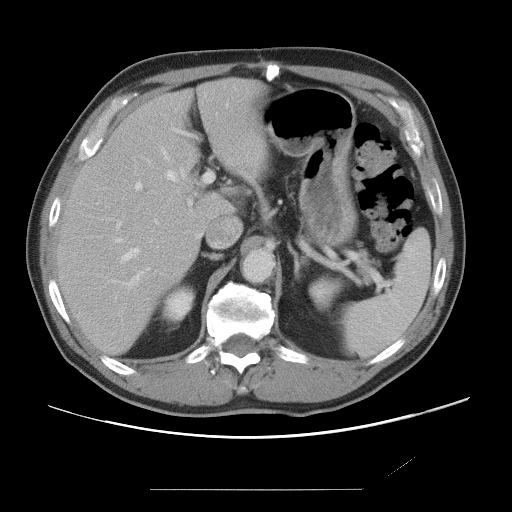
Contrast-enhanced abdominal CT, one axial slice. Position 47 of 87 along the scan axis. Intravenous contrast given. Soft-tissue window (W 400 / L 40 HU). 512 × 512 image matrix, field of view 406 × 406 mm. Male patient, age 74 years. Case-level facts recorded for this patient, not image findings: diagnosis: colorectal cancer liver metastases, imaged before liver resection; multiple liver metastases: yes; largest metastasis: 1.1 cm; disease in both lobes: no.
Annotated regions visible in this slice (manually delineated by an expert):
- hepatic veins: bounding box (x1, y1, x2, y2) in pixels: (116, 150, 185, 260)
- liver: (58, 78, 269, 353)
- planned liver remnant (the part of the liver to remain after resection): (58, 78, 269, 353)
- portal vein (with intrahepatic branches): (116, 130, 214, 288)